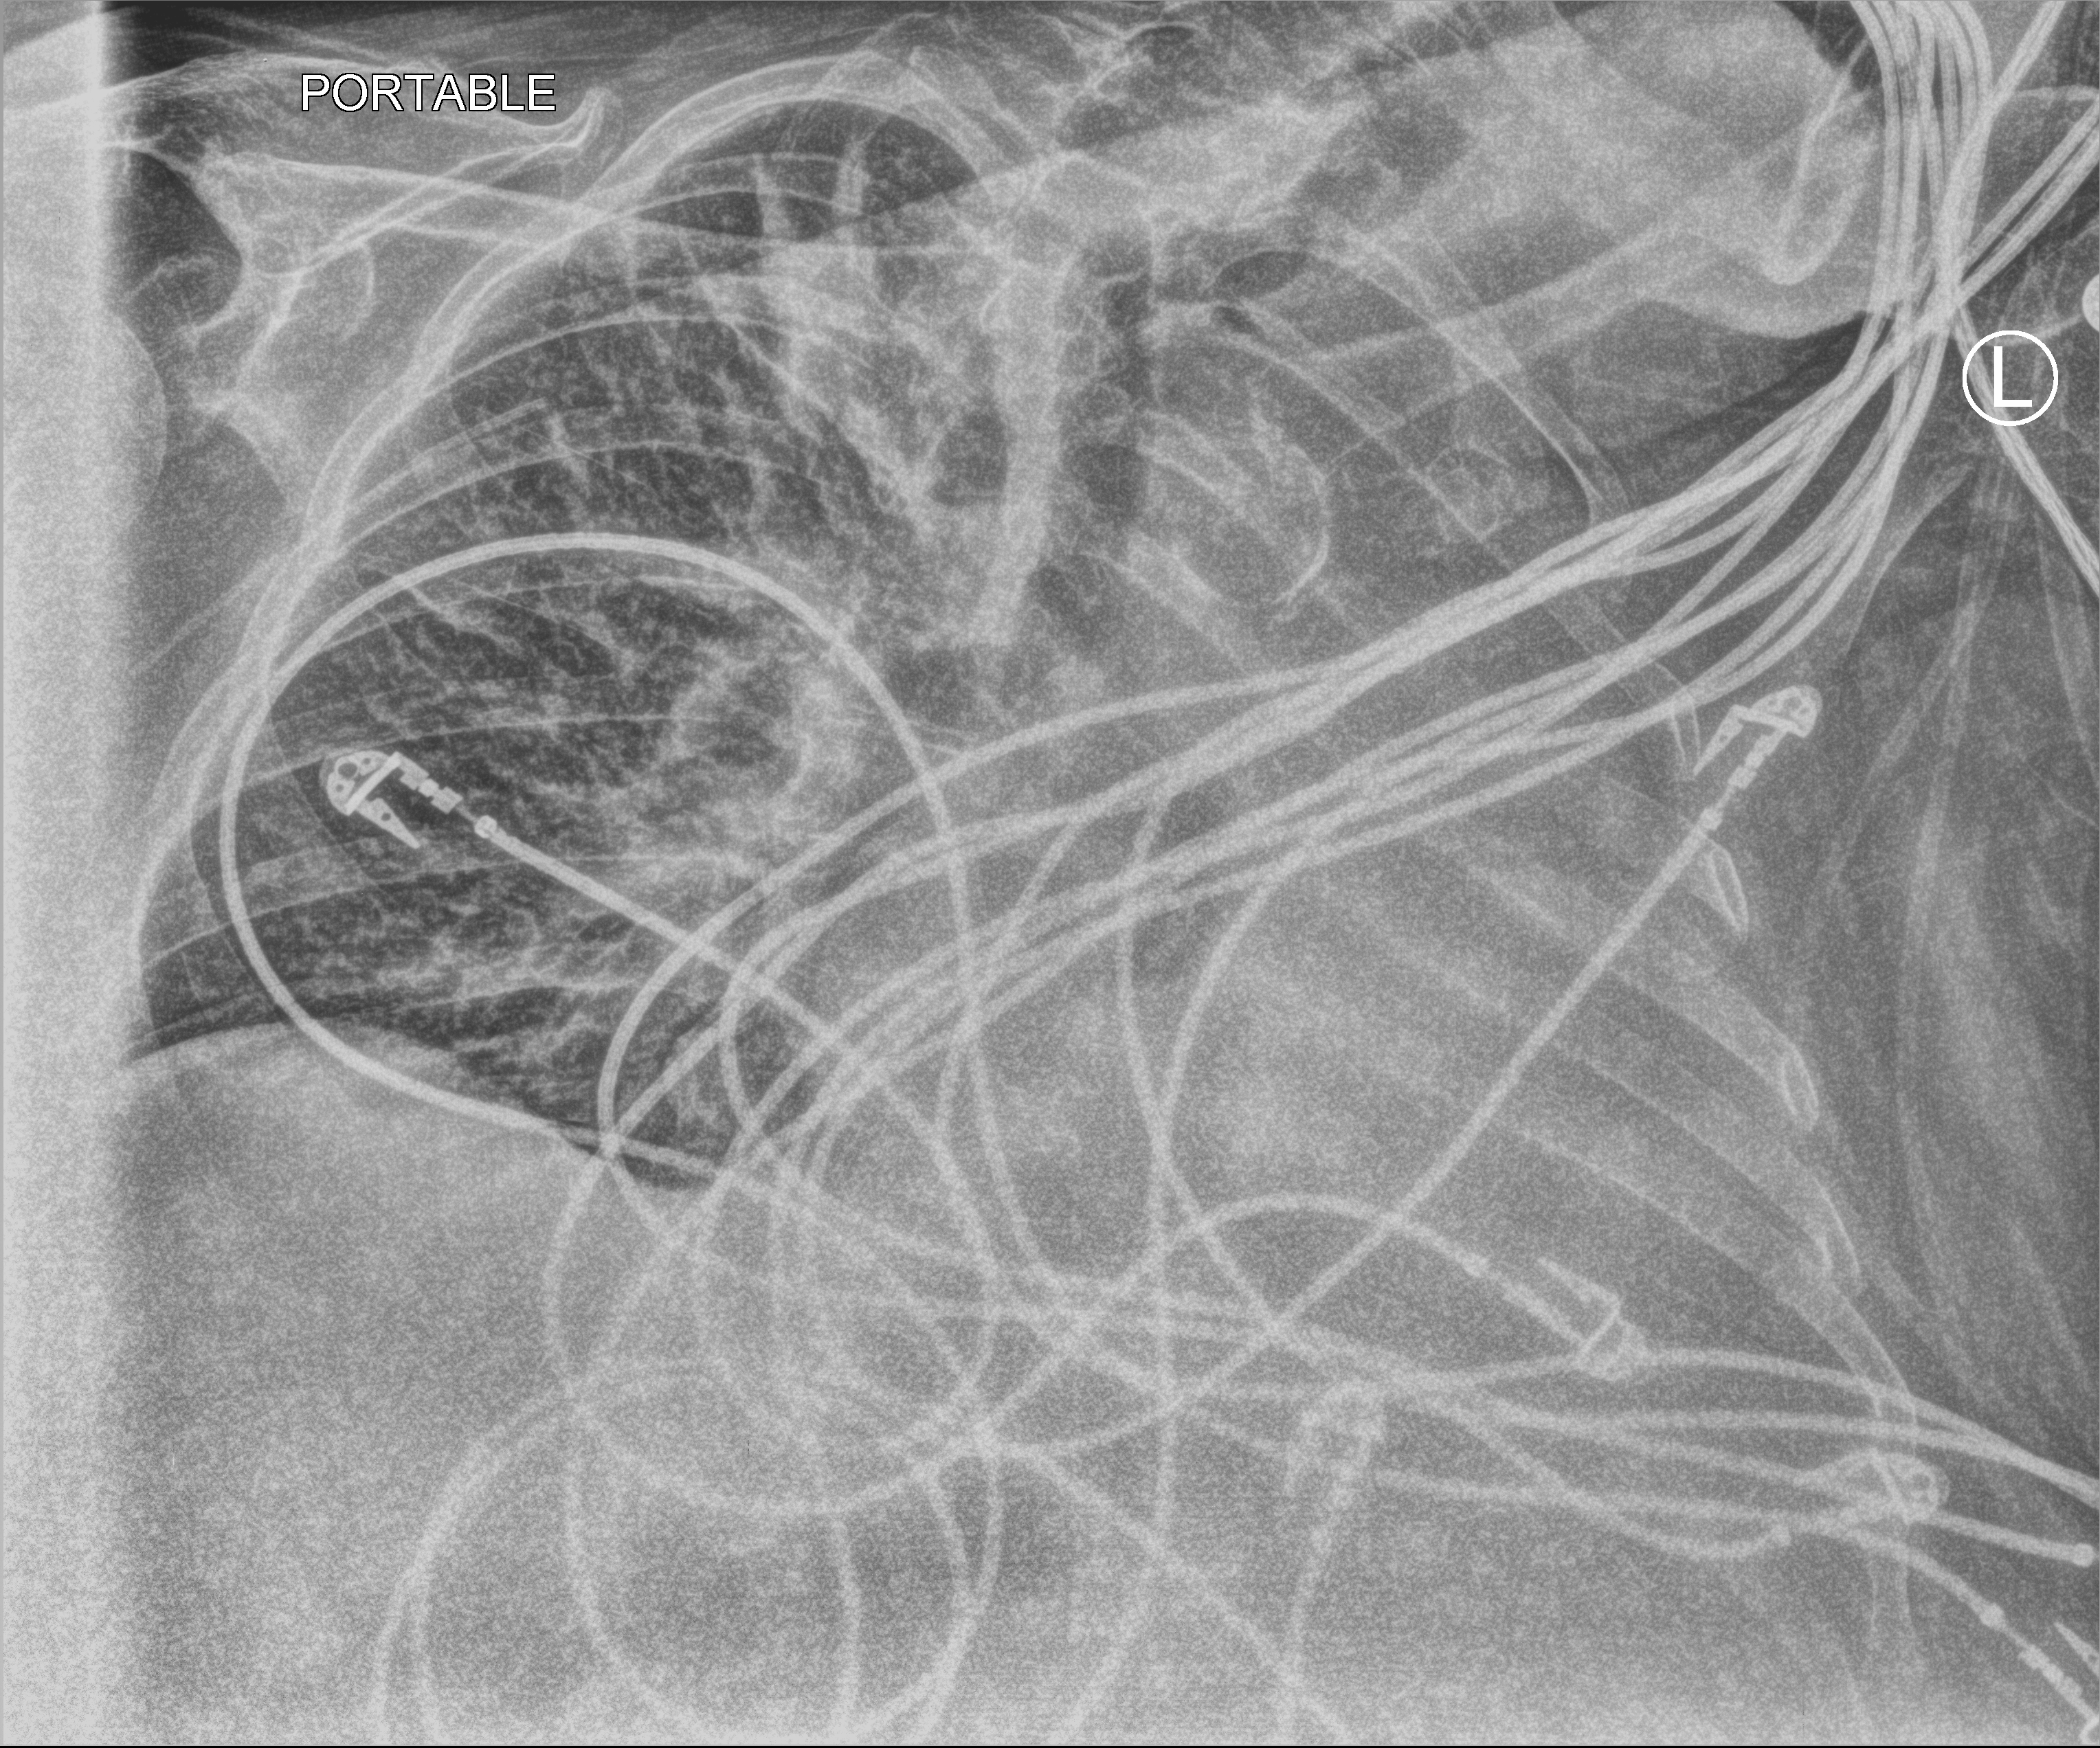
Bedside chest radiograph (computed radiography); anteroposterior (AP) projection. Female patient hospitalised with COVID-19, age 75–90 years.
Admission-level facts for this patient (not findings on this image; timing relative to this image not recorded): length of hospital stay: 5 days.